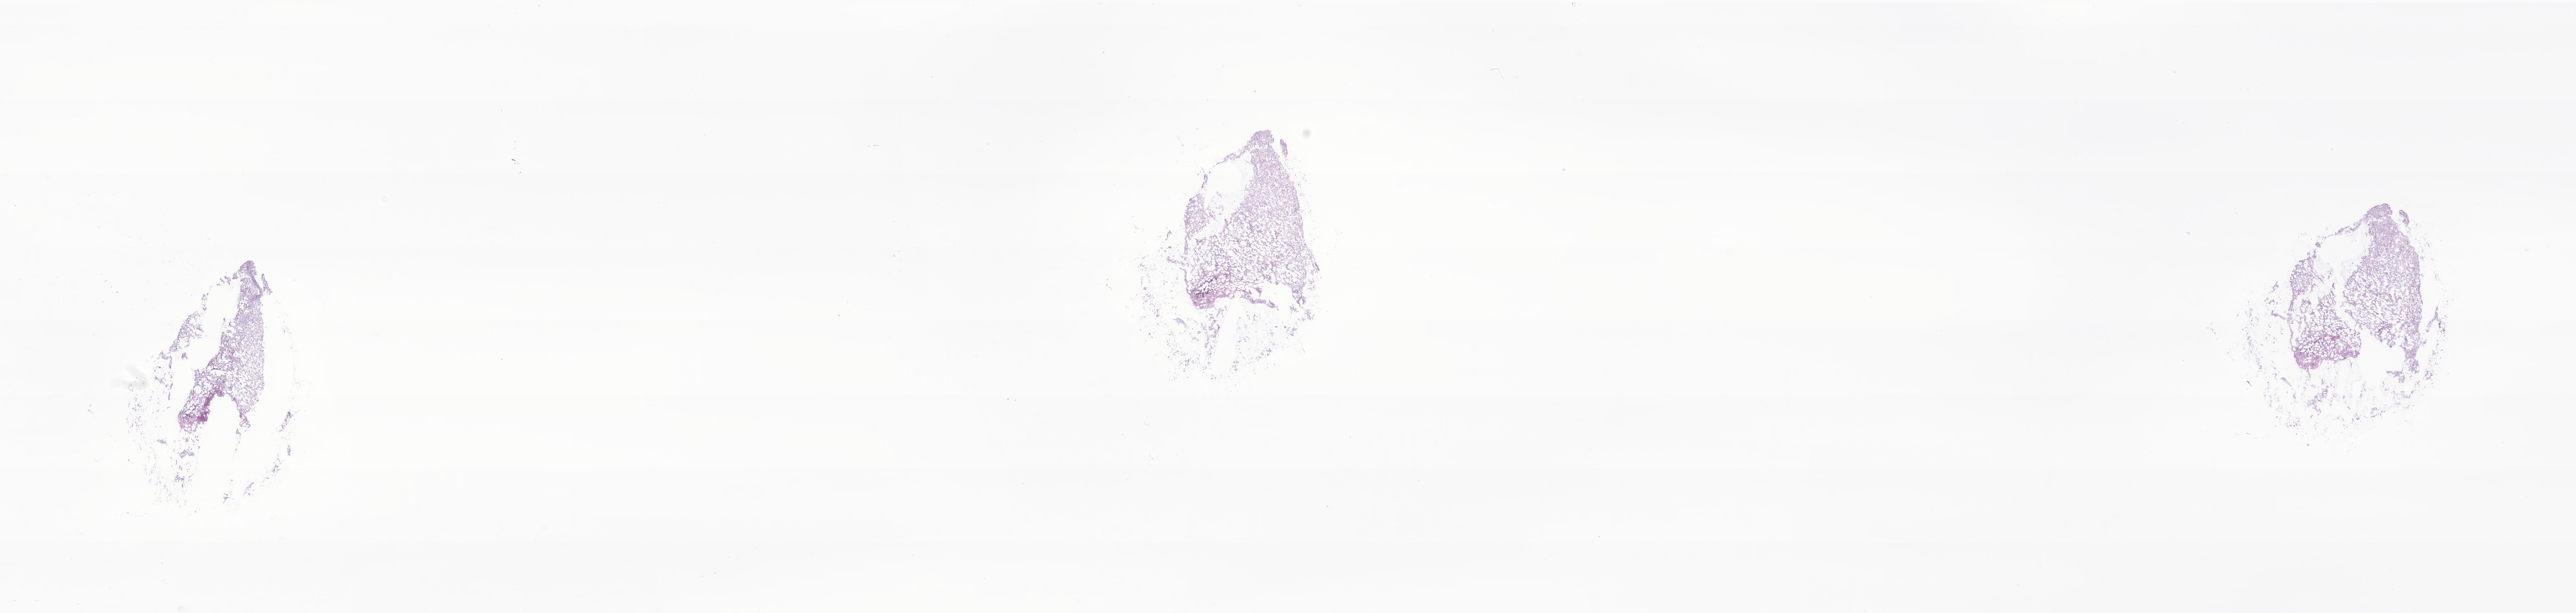
Digitized H&E-stained section of tumor tissue from the brain — shown as a low-resolution overview of the whole scanned area (about 37.3 x 8.9 mm). Frozen section. Female patient, age 696 days (about 1.9 years).
• recorded diagnosis: Neoplasm, malignant